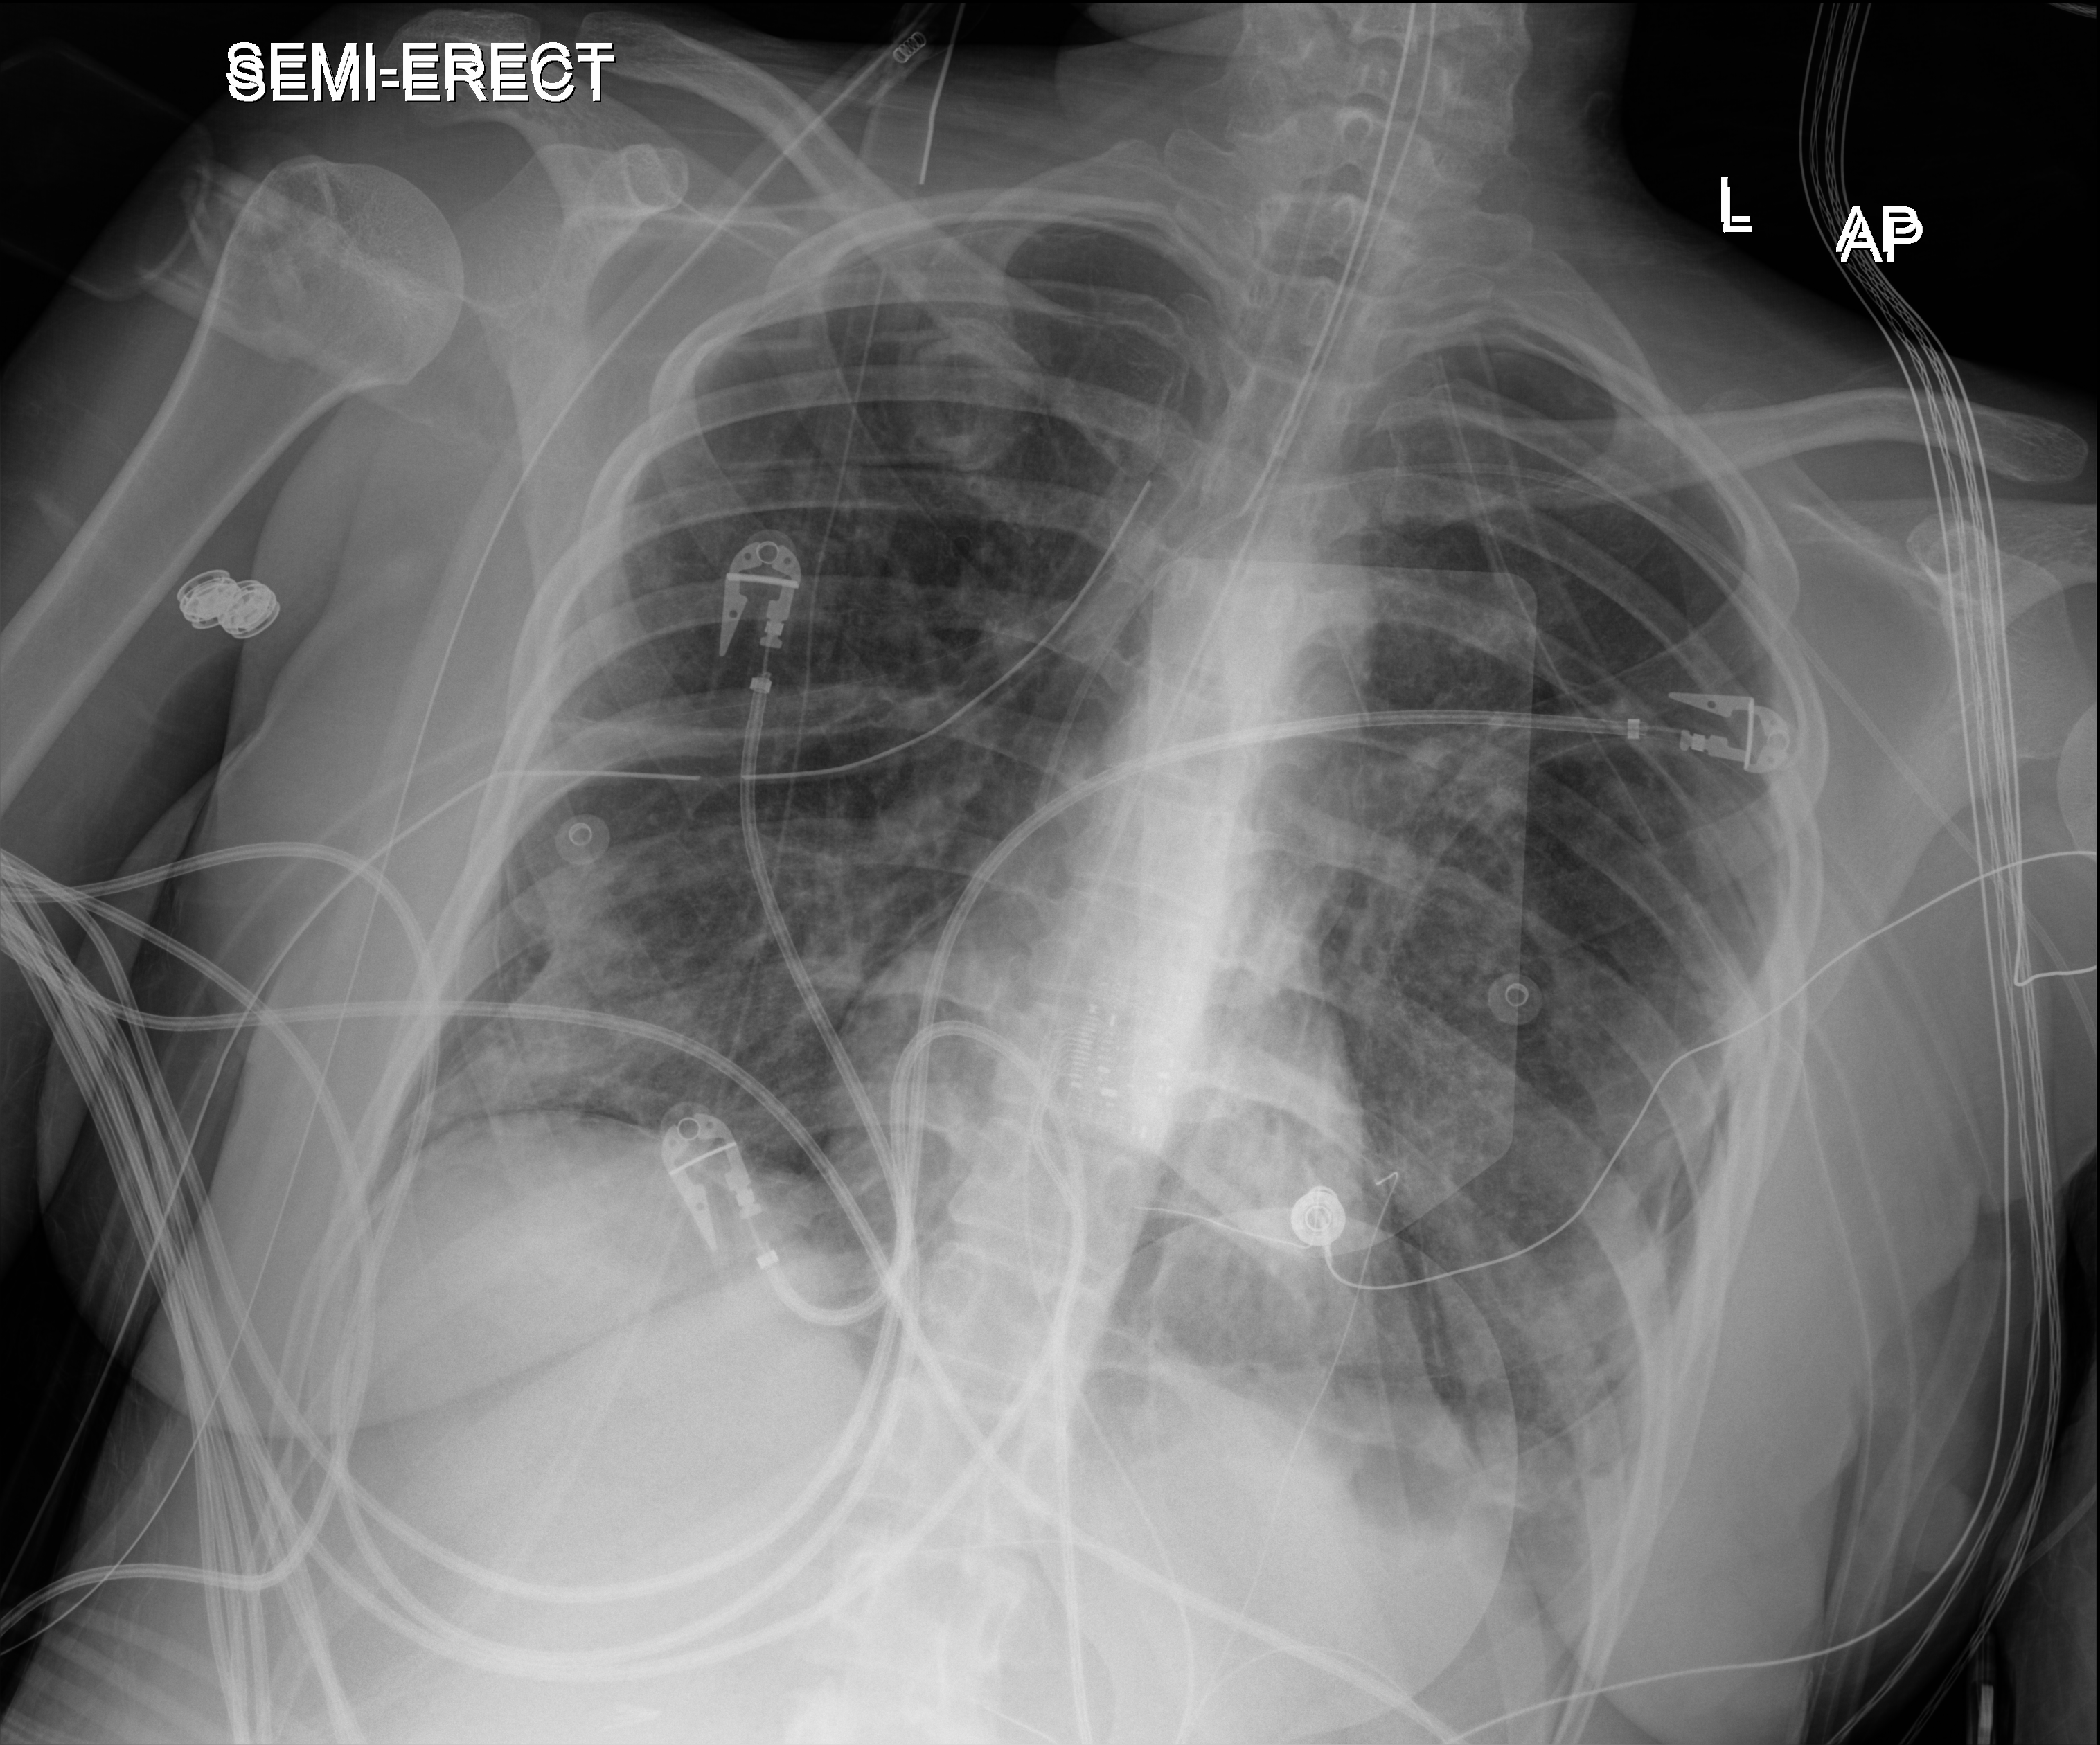
Chest X-ray (portable), anteroposterior (AP) projection. Patient hospitalised with COVID-19, aged 18–59 years.
From the hospital-stay record, not from the radiograph (when in the stay this image was taken is not recorded): COPD (admission record): no; smoking status (admission record): never.